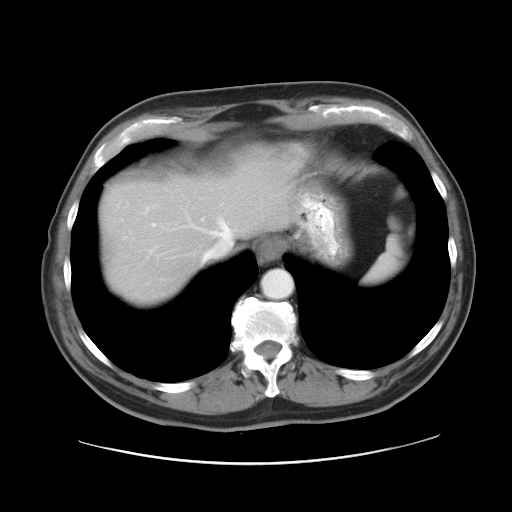
Contrast-enhanced abdominal CT, one axial slice. Position 24 of 28 along the scan axis. 120 kVp. Intravenous contrast given. Soft-tissue window (W 400 / L 40 HU). 7.5 mm slice thickness. 512 × 512 image matrix, field of view 402 × 402 mm. Male patient, age 74 years. Case-level facts recorded for this patient, not image findings: diagnosis: colorectal cancer liver metastases, imaged before liver resection; multiple liver metastases: no; largest metastasis: 5 cm; disease in both lobes: no.
Outlined on this slice (outlined manually by an expert reader):
- hepatic veins: bounding box <149,220,232,260> (left, top, right, bottom; pixels)
- liver: <103,160,282,300>
- planned liver remnant (the part of the liver to remain after resection): <103,185,212,301>